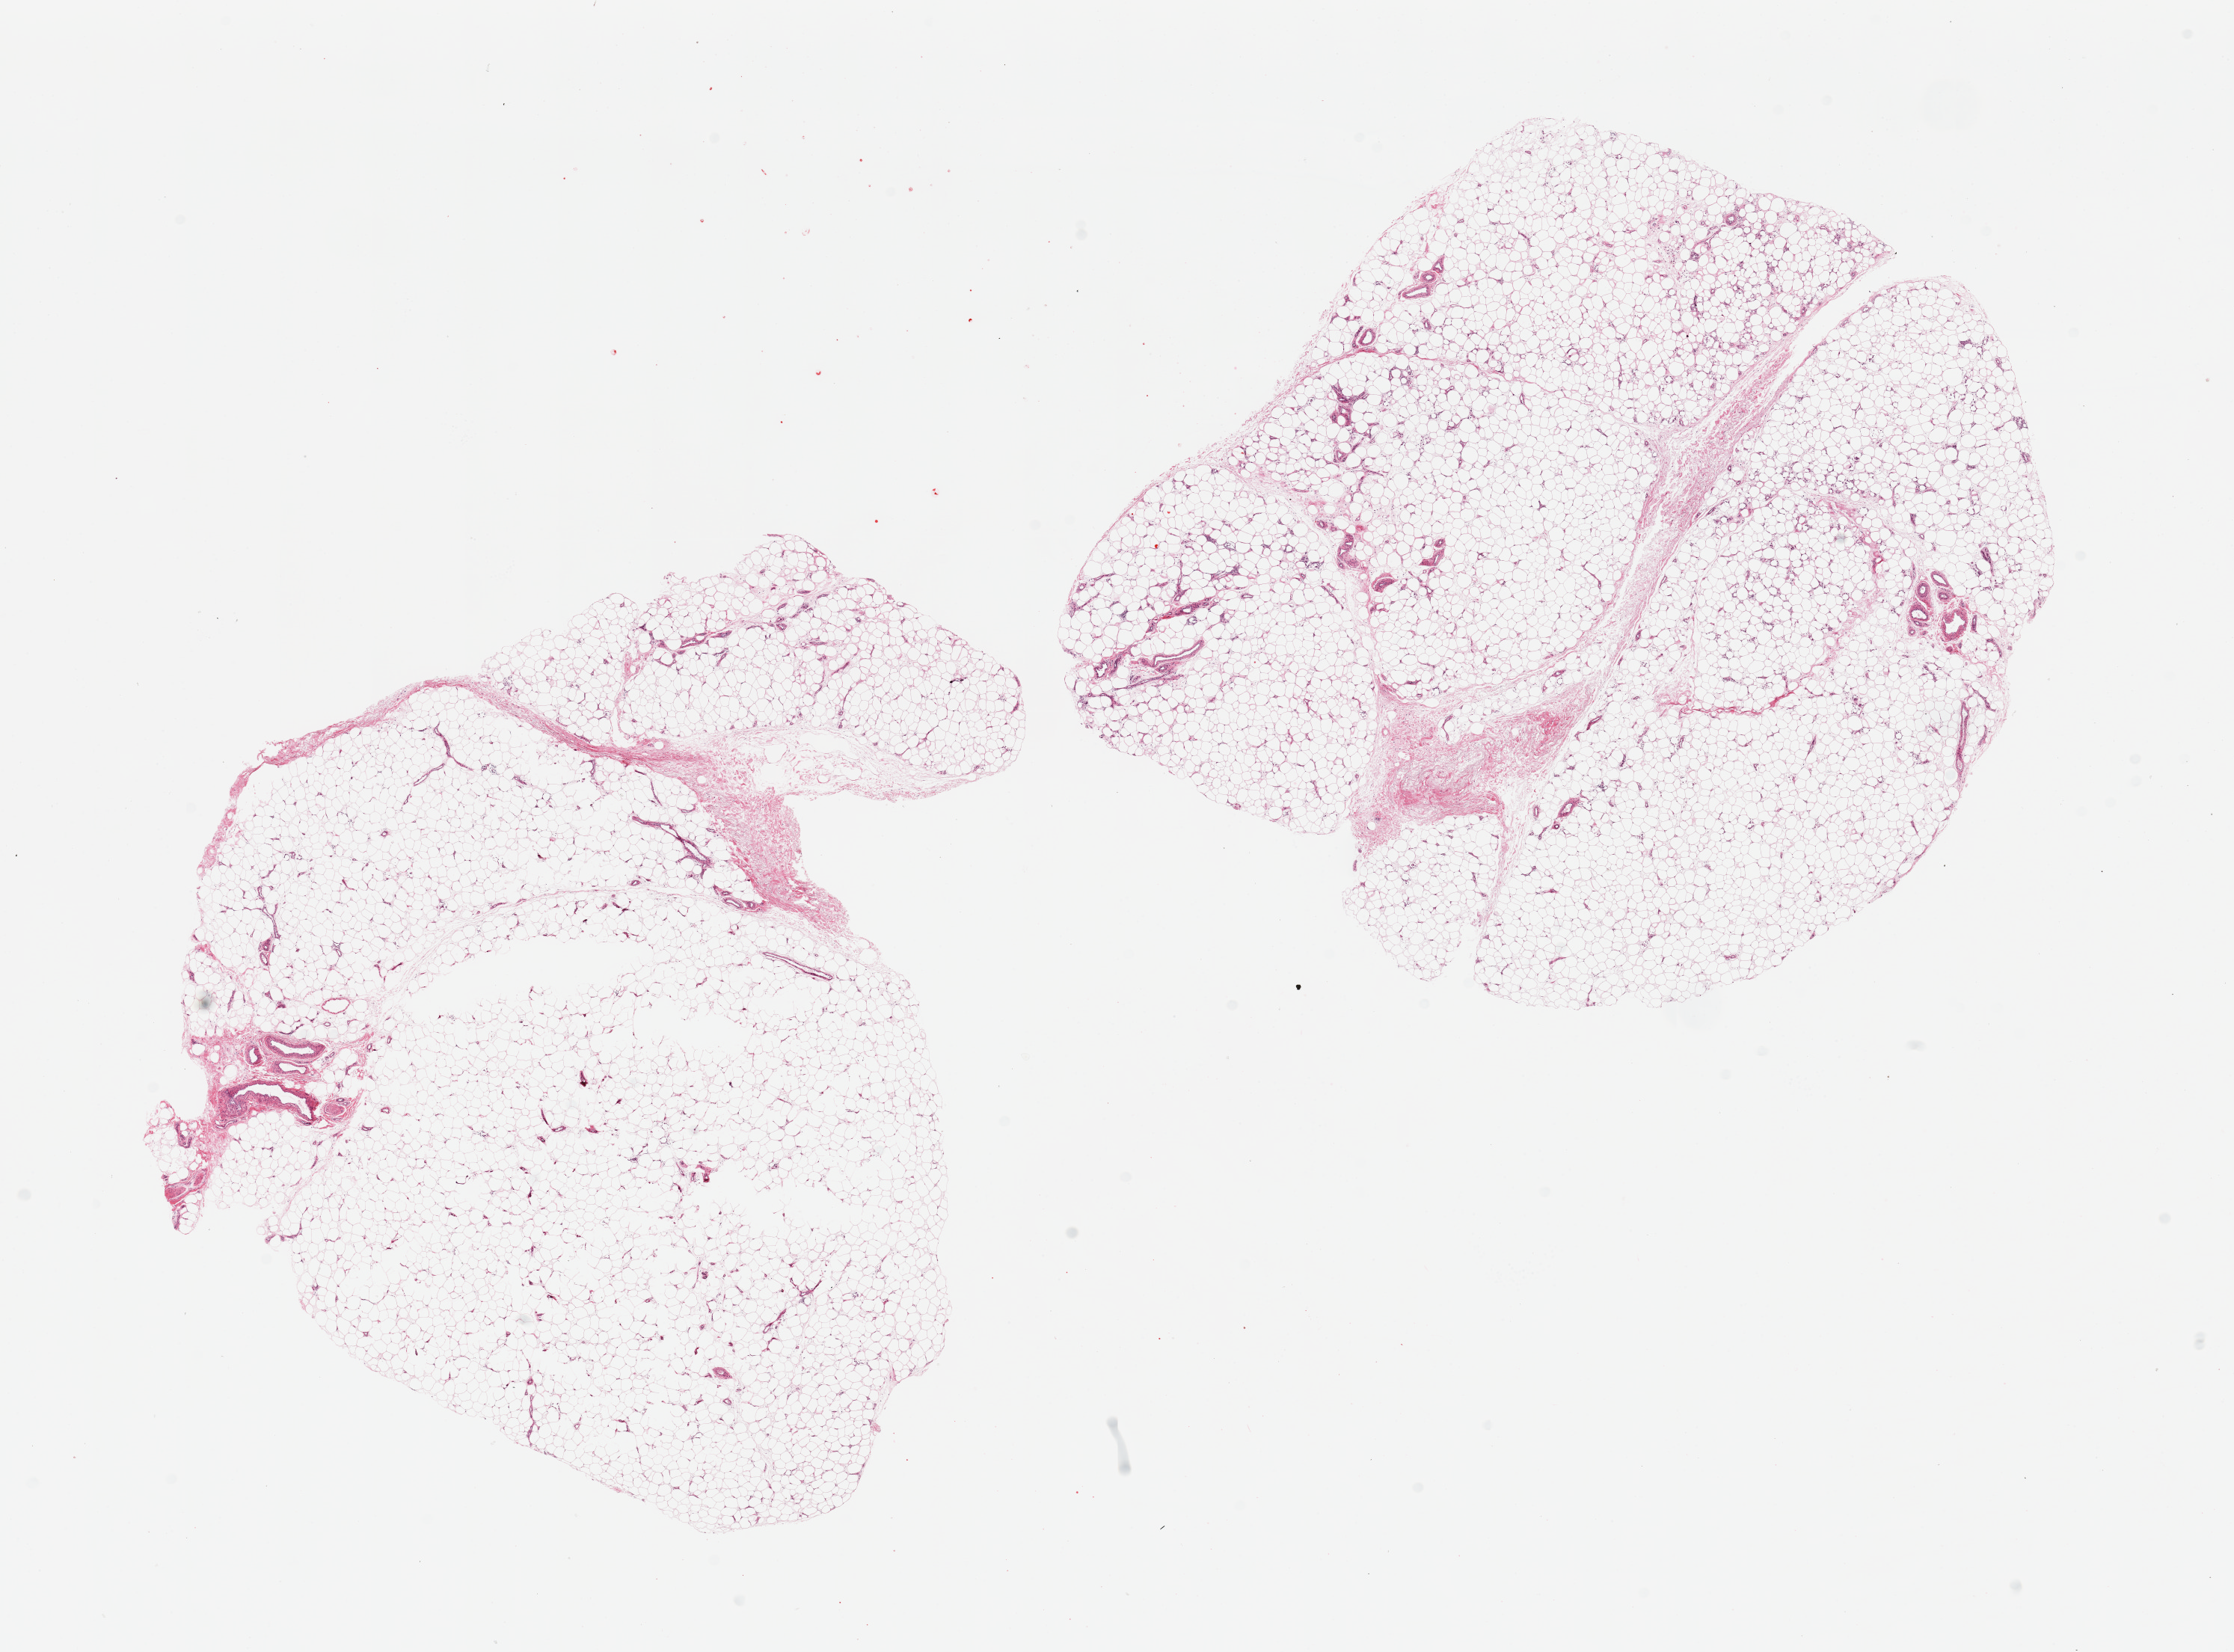
Digitized H&E-stained section, brightfield, shown as a low-resolution overview of the whole scanned area (about 23.6 x 17.5 mm, from a 20x scan), PAXgene-fixed, paraffin-embedded tissue, target tissue: adipose tissue, tissue donor sample. Male donor.
Pathologist's review note for this sample: 2 pieces.